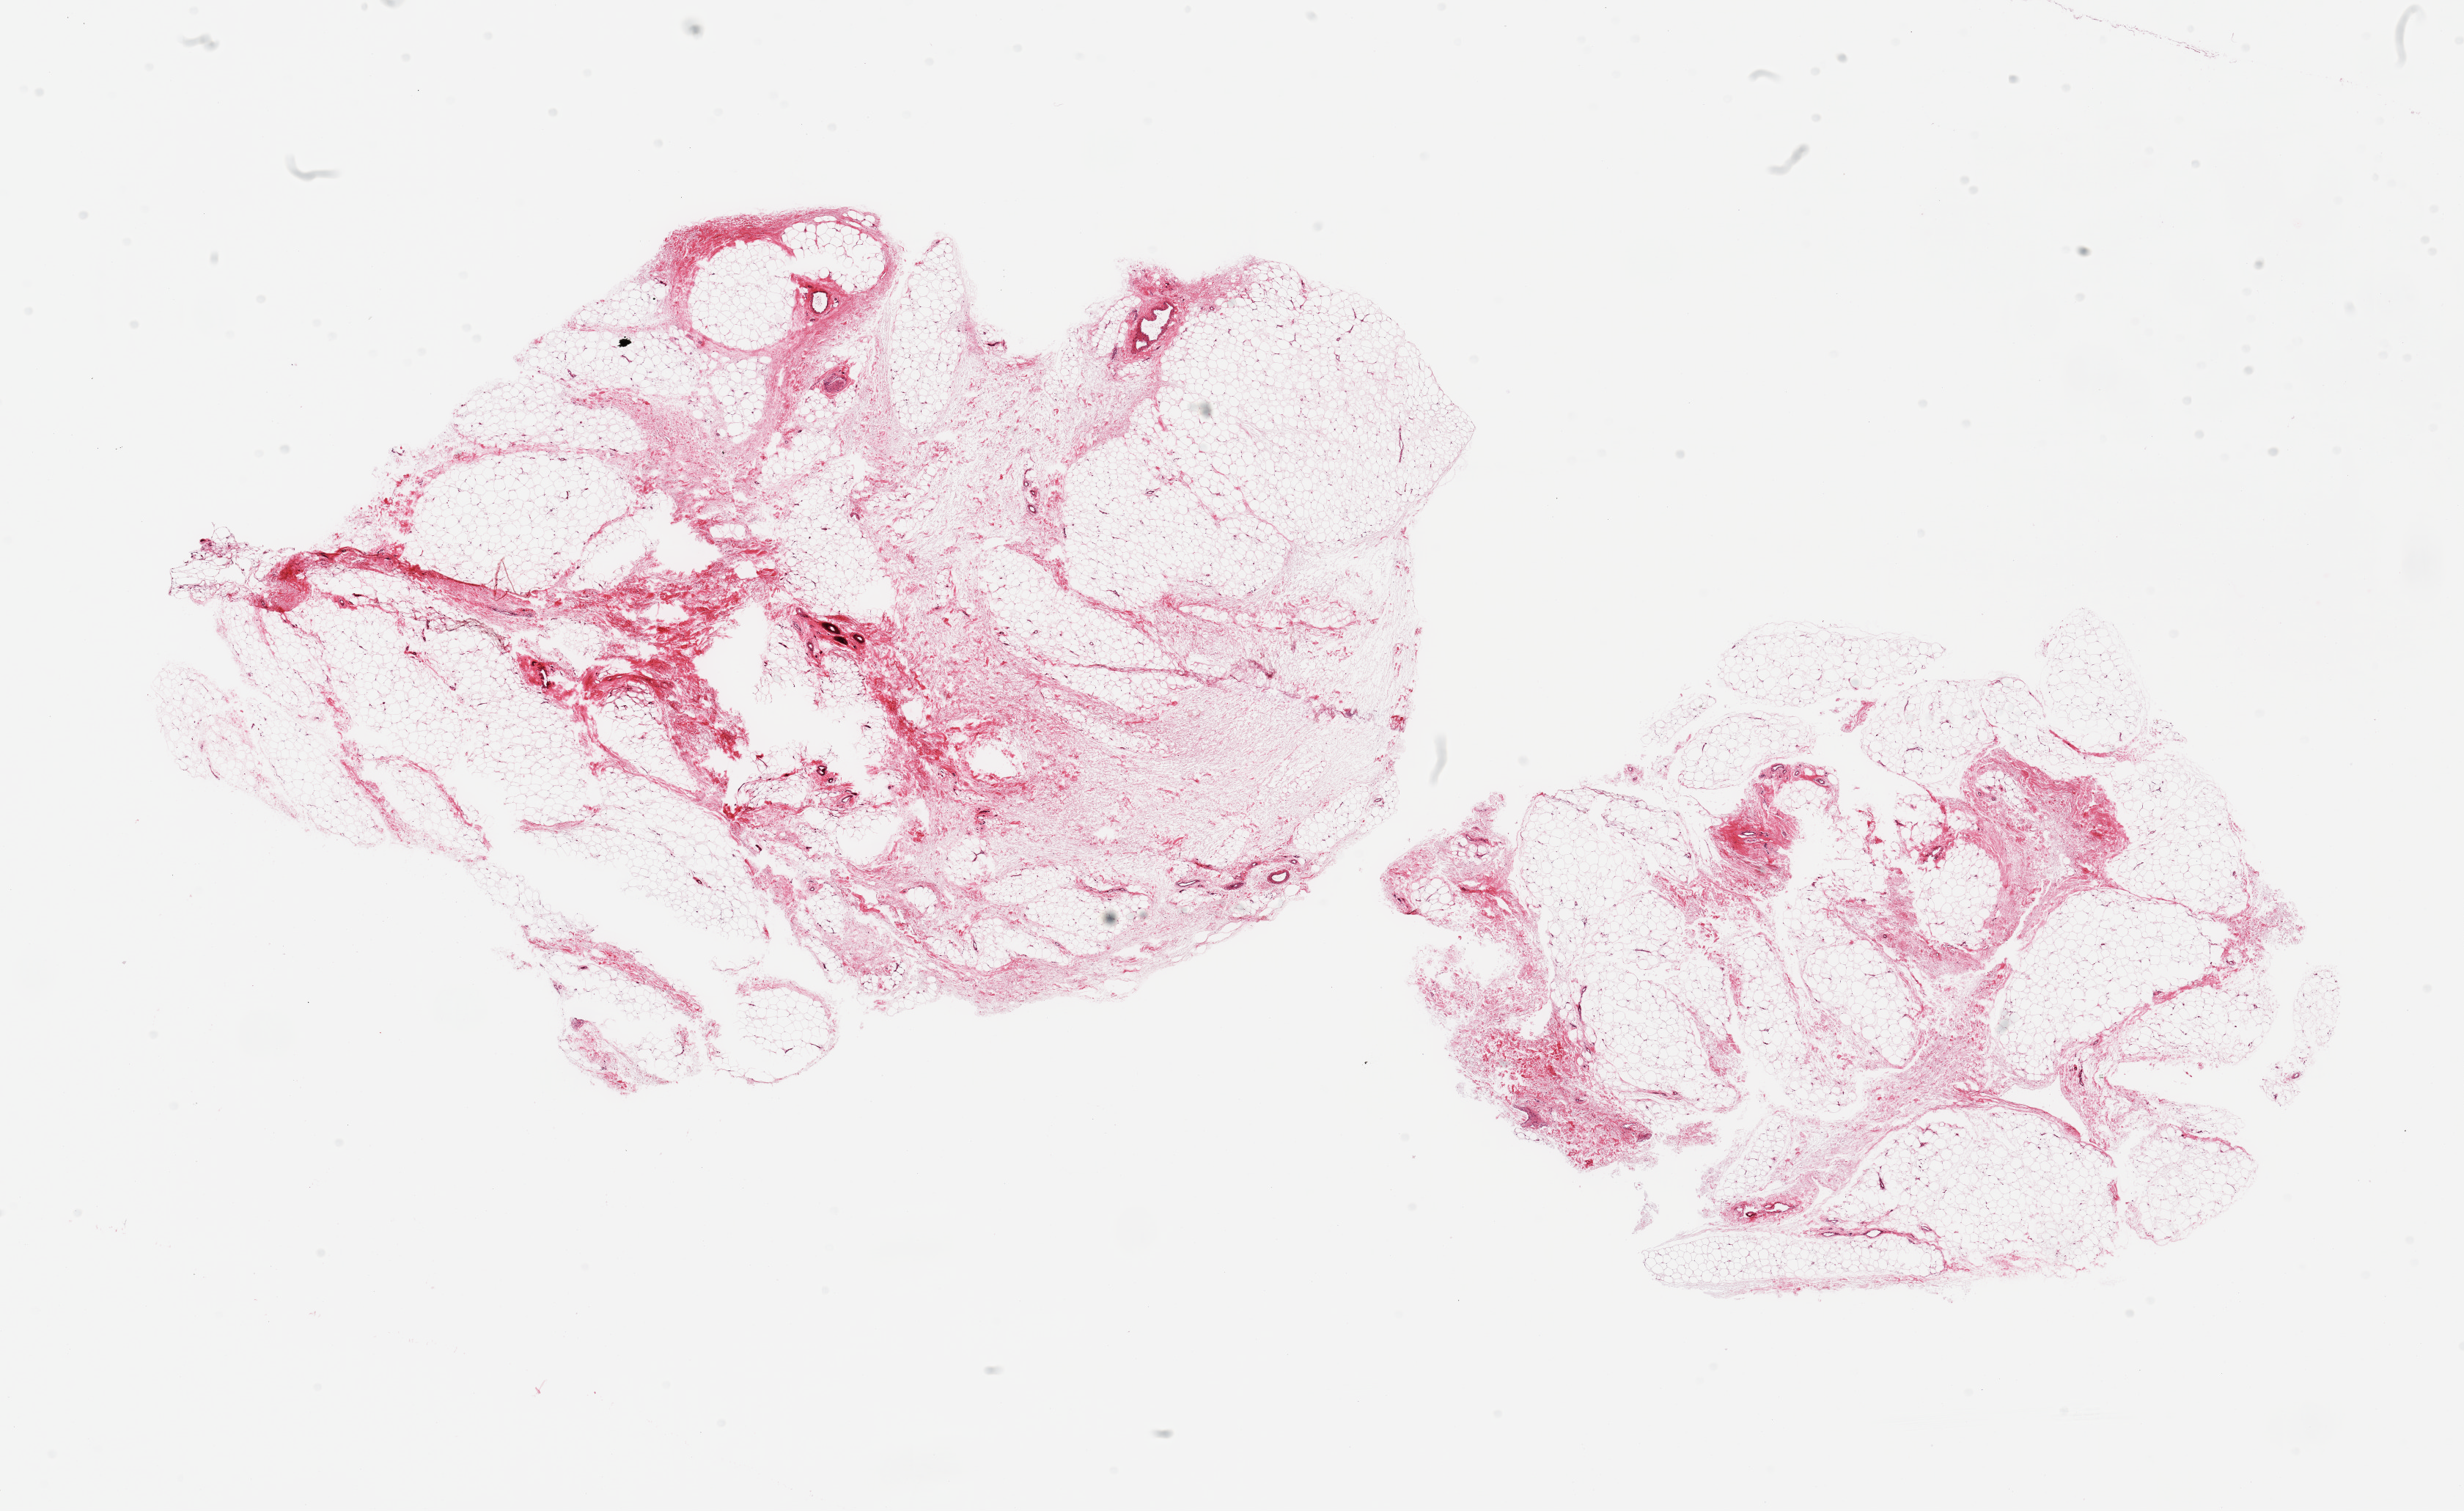
Whole-slide image, hematoxylin and eosin (H&E) stain, brightfield — whole scanned area (about 26.6 x 16.3 mm) shown as a low-resolution overview, PAXgene-fixed, paraffin-embedded tissue, section of adipose tissue (target tissue), donor tissue sample. Male donor.
Pathologist's review note for this sample: 2 pieces, fascia/vascular elements are ~10-15% of tissue.